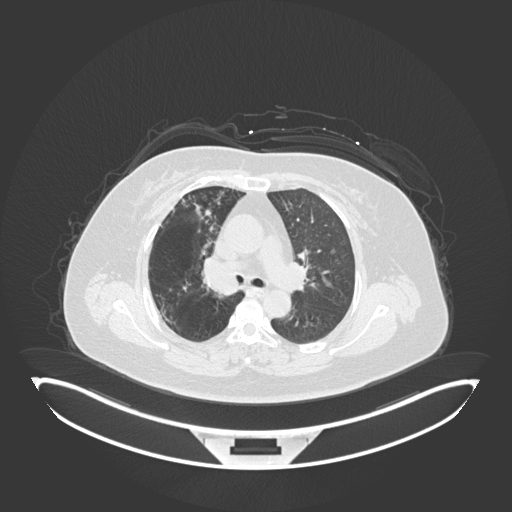
Chest CT, one axial slice; reconstruction kernel B30f; lung window (W 1500 / L -600 HU); 1 mm slice thickness; 512 × 512 image matrix. Patient: female, 60 years. From the clinical record (not read from this slice): clinical TNM (as recorded): T1c N0 M0; histopathological grade: G1-G2.
Annotated regions visible in this slice (bounding box drawn by a radiologist):
- lung tumour (recorded histology: squamous cell carcinoma): bounding box <198,251,240,299> (left, top, right, bottom; pixels)